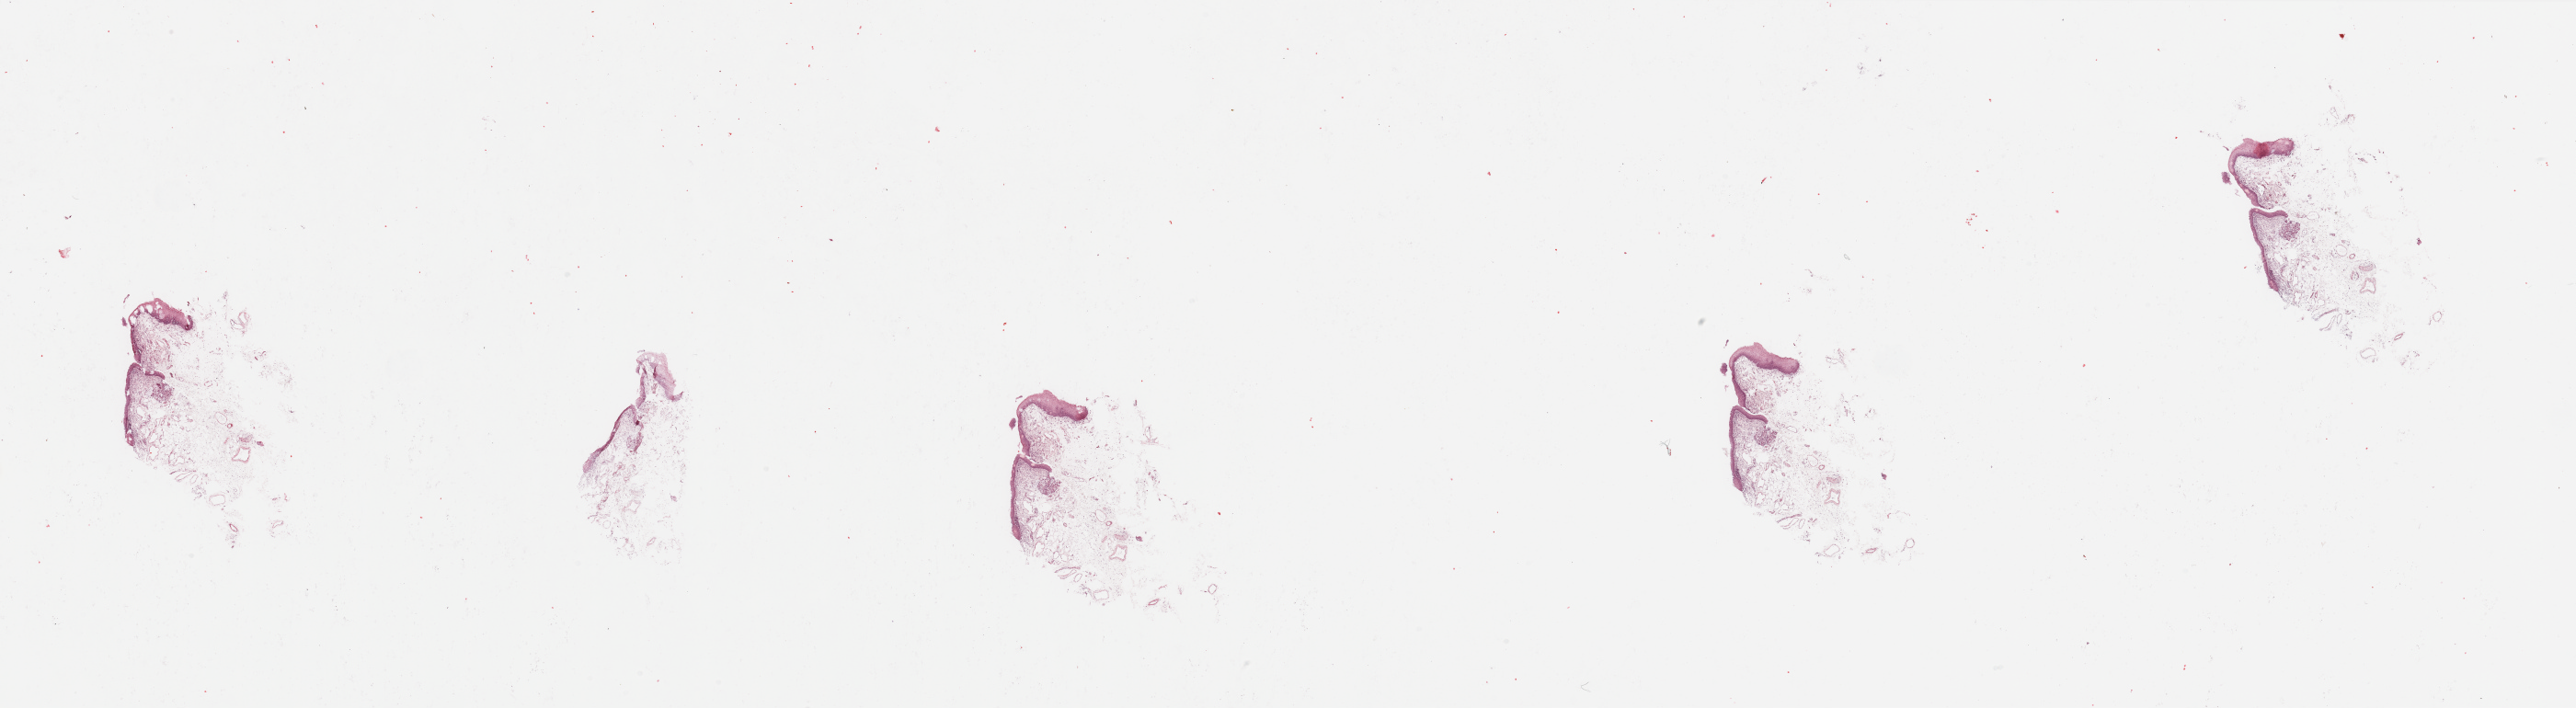
H&E whole-slide image — low-resolution overview of the scanned area, about 44.3 x 12.2 mm (slide scanned at 20x); normal (non-tumour) tissue sample, head and neck. Male, 68 y/o.
This section: normal (non-tumour) tissue from the same patient. Patient diagnosis: Squamous cell carcinoma, NOS (larynx, NOS).